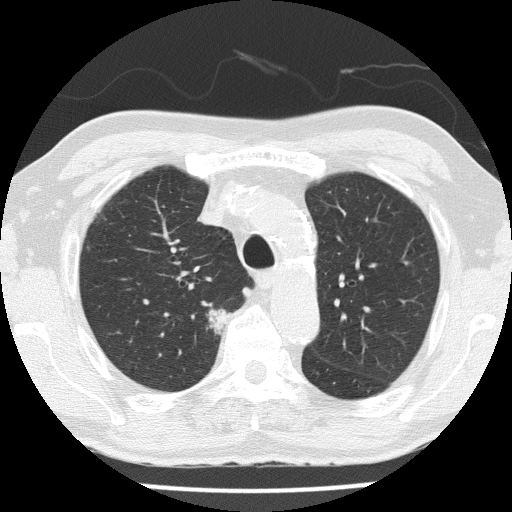
Chest CT (low-dose screening protocol), one axial image. Third screening round (two years after baseline). Lung window (W 1500 / L -600 HU). 2 mm slice thickness. Lung (sharp) reconstruction kernel (FC51). Slice 44 of 153 in the series. Male, age 72 years at enrolment. Current smoker at enrolment.
Lesion marked by an expert reader, box from (x=188, y=295) to (x=241, y=347) px. Screening reader's record for this exam (one nodule recorded; not confirmed to be the boxed lesion): non-calcified nodule or mass ≥4 mm, right upper lobe, 14 × 14 mm, spiculated (stellate) margins, soft tissue attenuation, pre-existing on the prior screen: yes; interval growth: yes. Official screen result: positive, other. Later outcome: lung cancer diagnosed 67 days after this screen — squamous cell carcinoma, NOS, right upper lobe, moderately differentiated (G2), stage IIA (AJCC 6th edition), 25 mm at pathology.